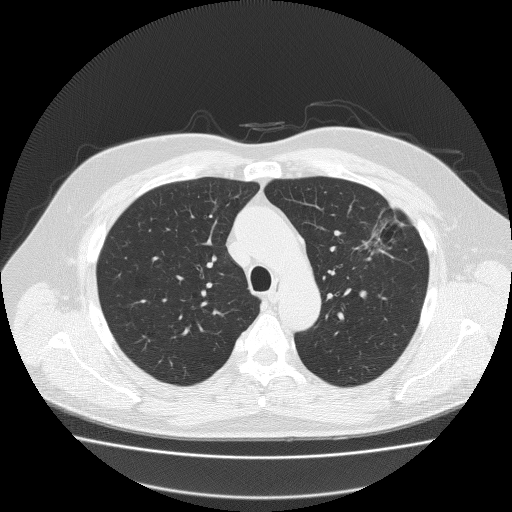
Chest CT (low-dose screening protocol), one axial image, first (baseline) screen, lung window (W 1500 / L -600 HU), lung (sharp) reconstruction kernel (FC51). Male, age 62 years at enrolment.
Expert reader's lesion annotation, bounding box (x1, y1, x2, y2) in pixels: (357, 198, 425, 260). The exam's reader record, not a measurement of the box and not confirmed to be the same lesion: non-calcified nodule or mass ≥4 mm, left upper lobe, 18 × 8 mm, spiculated (stellate) margins, soft tissue attenuation. Official screen result: positive, change unspecified: nodule(s) >= 4 mm or enlarging nodule(s), mass(es), or other non-specific abnormalities suspicious for lung cancer. Participant outcome: lung cancer diagnosed 49 days after this screen — bronchiolo-alveolar adenocarcinoma, NOS, left upper lobe, well differentiated (G1), stage IA (AJCC 6th edition), 25 mm at pathology.